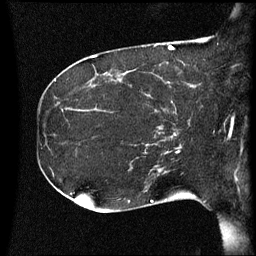
Breast MRI (dynamic contrast-enhanced), one sagittal slice. Slice 21 of 60 in the series (ordered by position). Dynamic contrast-enhanced series, image 2 of 3 at this slice position (ordered by acquisition). 1.5 T. TE 4.2 ms, TR 8.4 ms. 256 × 256 image matrix, field of view 220 × 220 mm. Female patient, age 41 years. Case-level facts recorded for this patient, not image findings: setting: breast cancer imaged before/during neoadjuvant chemotherapy; receptor status: HER2-positive.
Annotated regions visible in this slice (semi-automatic segmentation, software-assisted and operator-edited):
- analysis volume of interest (the breast-tissue region the enhancement analysis was run in; not a lesion): bounding box <122,80,197,125> (left, top, right, bottom; pixels)
- tumour enhancement mask (voxels above the 70 % enhancement threshold inside the analysis volume of interest): <191,86,195,87>